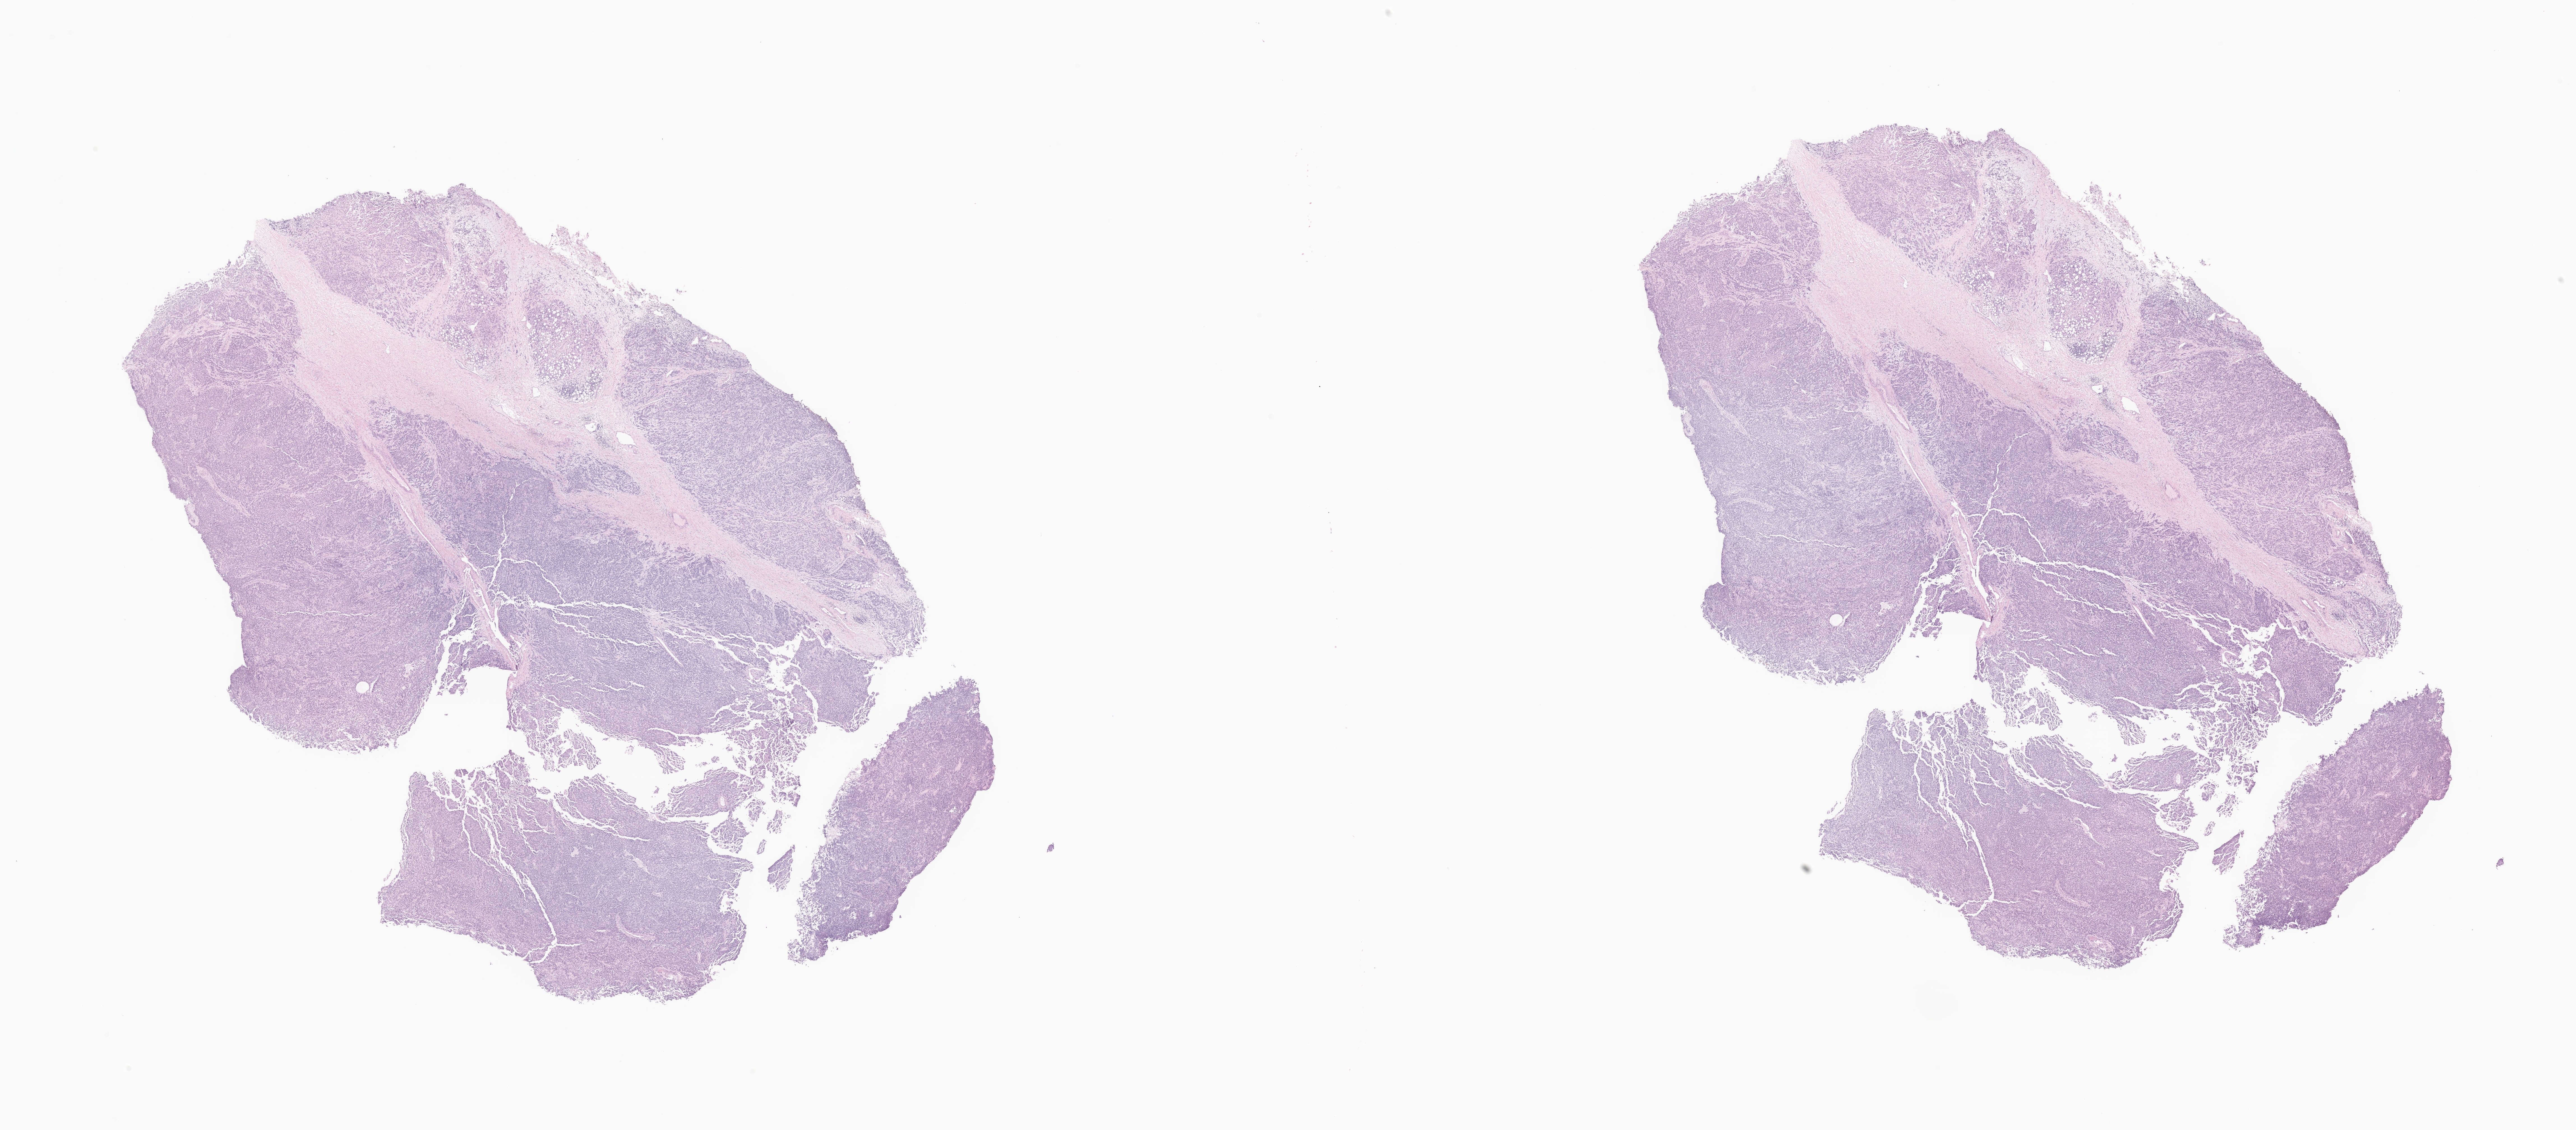
Haematoxylin and eosin whole-slide image of tumor tissue from the renal pelvis, shown as a low-resolution overview of the whole scanned area (about 38.7 x 17.0 mm), FFPE section. Patient male; age 40 months (3 years 4 months).
Diagnosis: Neuroblastoma, NOS.